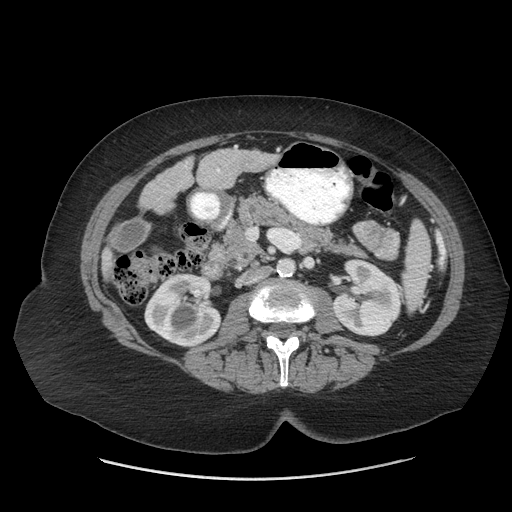
Contrast-enhanced abdominal CT (liver protocol), one axial slice; position 17 of 69 along the scan axis; soft-tissue window (W 400 / L 40 HU); 2.5 mm slice thickness; 512 × 512 image matrix. From the clinical record (not read from this slice): diagnosis: hepatocellular carcinoma (patient treated with transarterial chemoembolisation; whether this scan precedes or follows treatment is not stated here); TNM stage (as recorded): Stage-IIIB; Child-Pugh class: A.
Annotated regions visible in this slice (semi-automatic segmentation, software-assisted and operator-edited):
- liver parenchyma outside the tumour (the mass and vessels are separate outlines, so this box may not span the whole liver): bounding box [x1, y1, x2, y2] px = [102, 147, 277, 279]
- liver vessels: [217, 168, 220, 173]